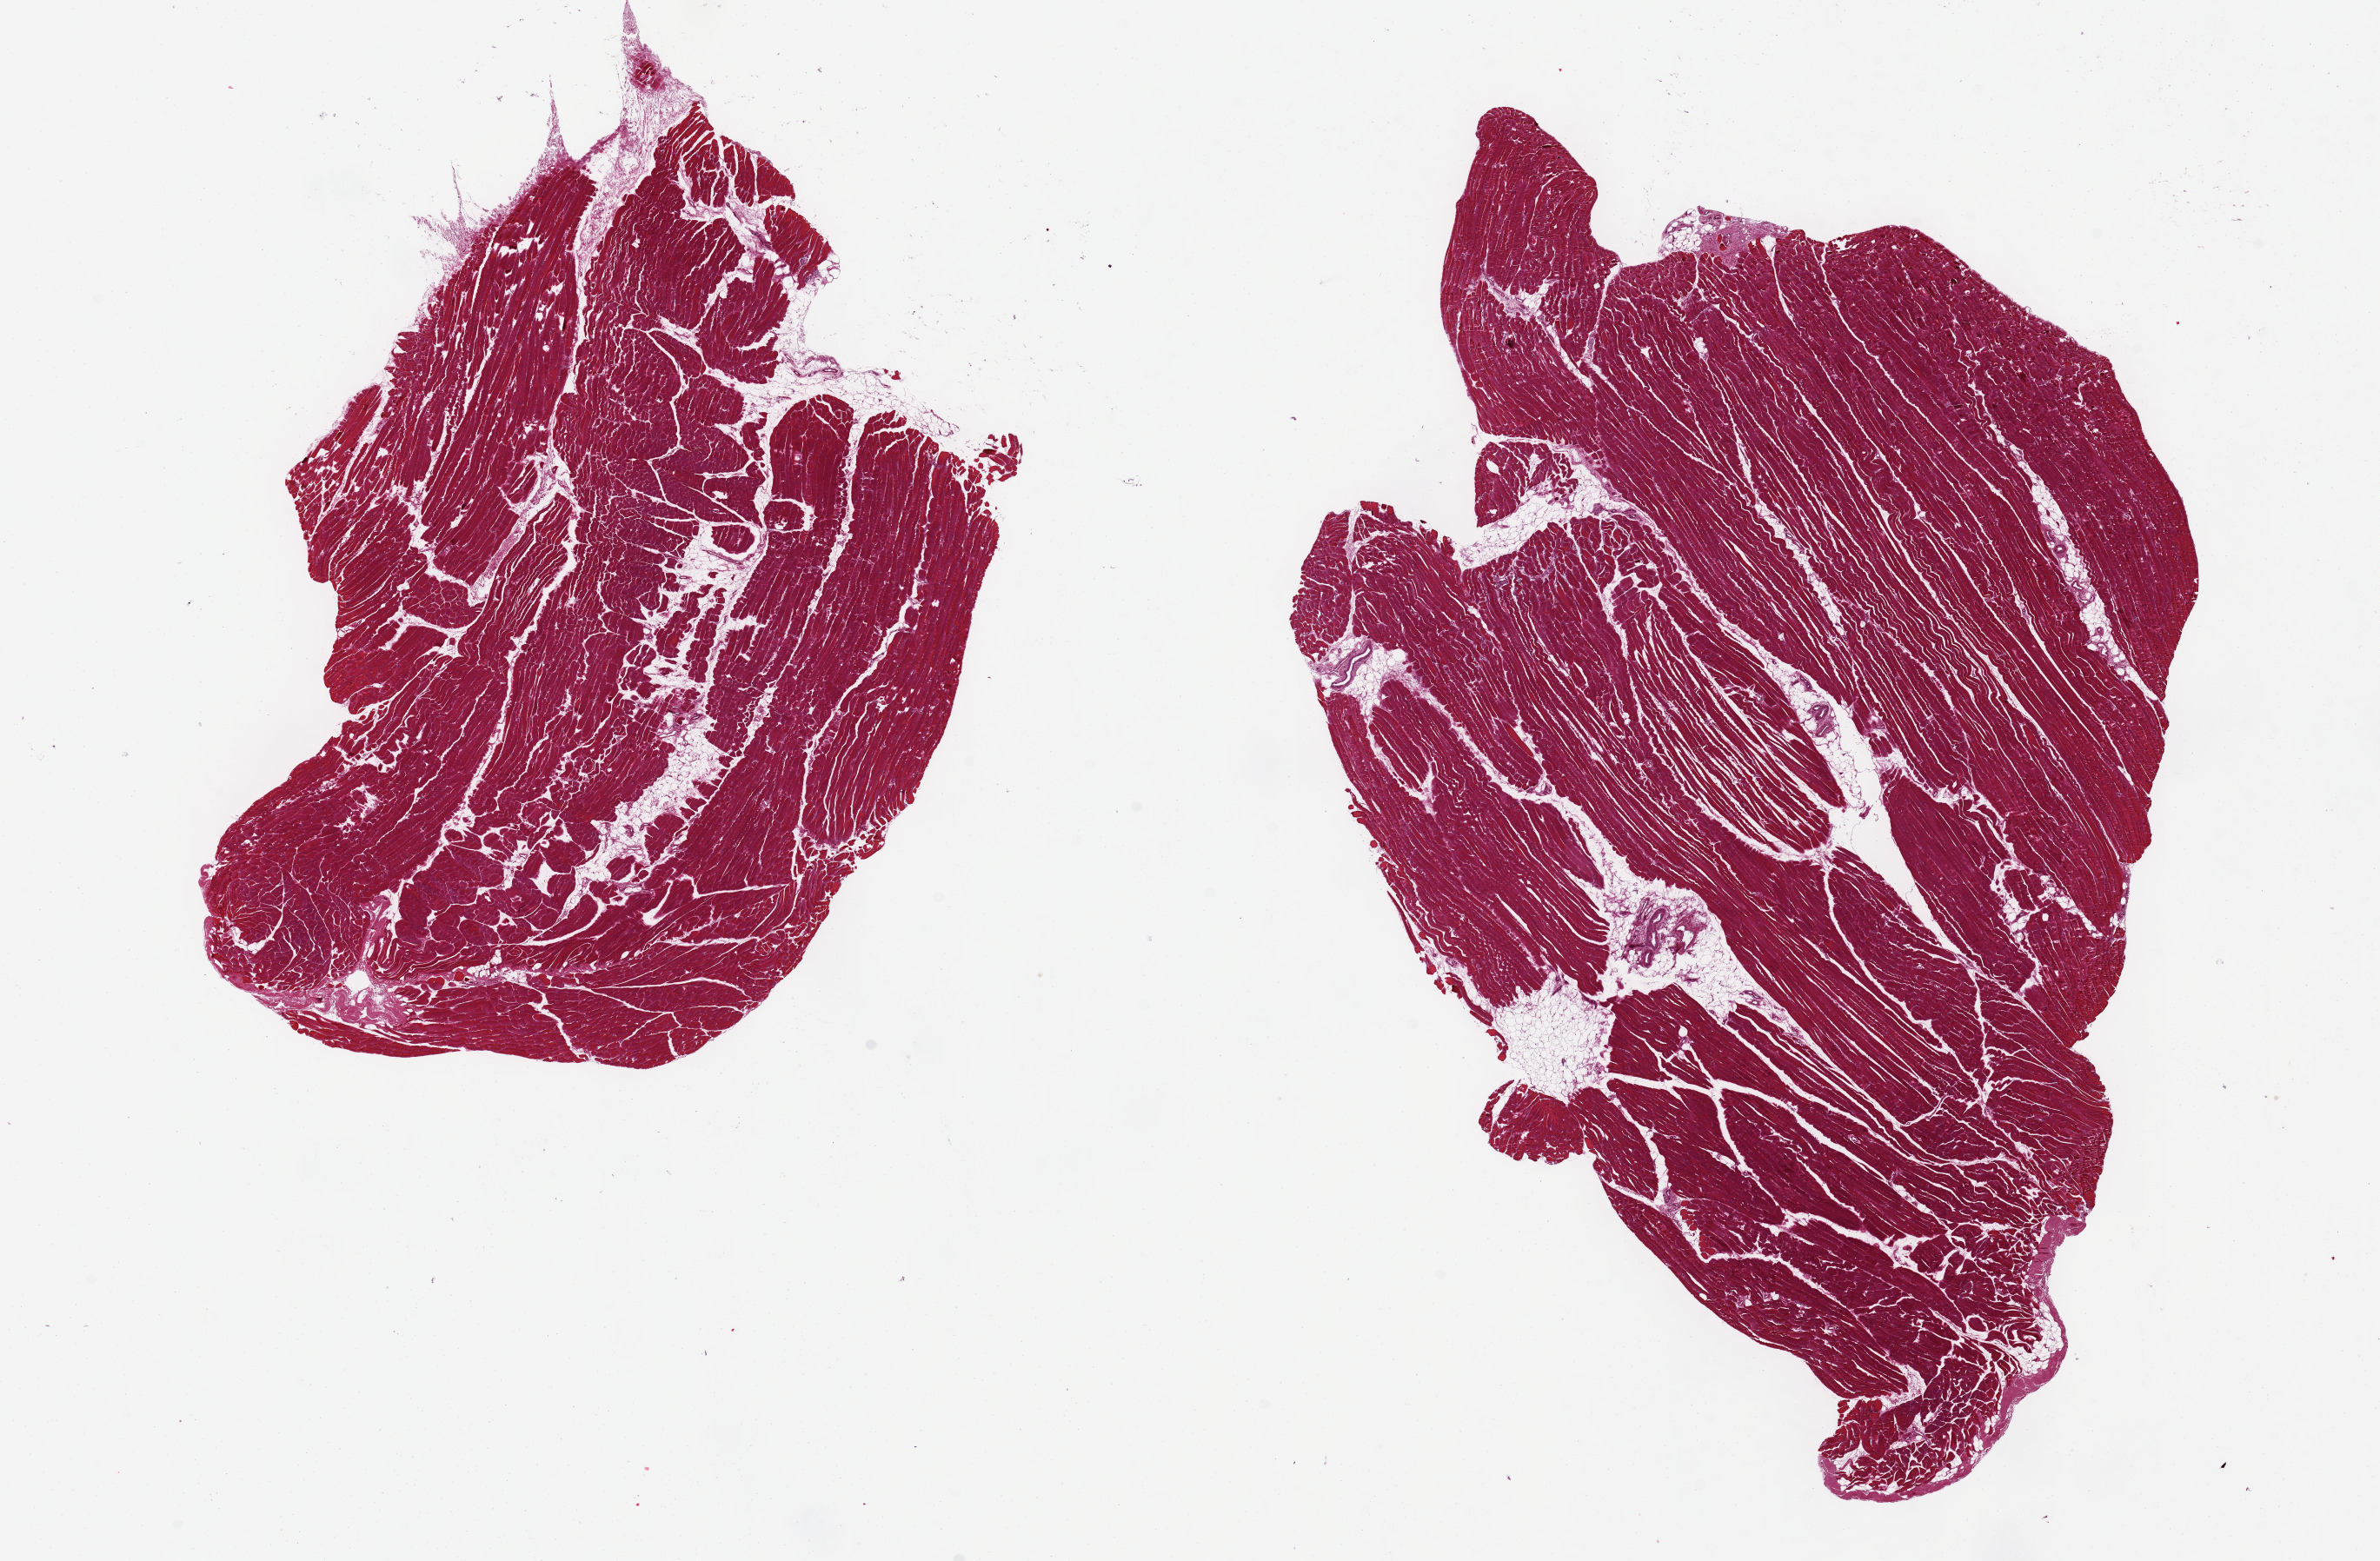
Whole-slide image, H&E stain — shown as a low-resolution overview of the whole scanned area (about 21.7 x 14.2 mm, acquisition: 20x scan). PAXgene-fixed, paraffin-embedded tissue. Target tissue: skeletal muscle. Donor tissue sample.
• reviewer comment on this tissue sample: 2 aliquots. Minimal (<5%) interstitial fat